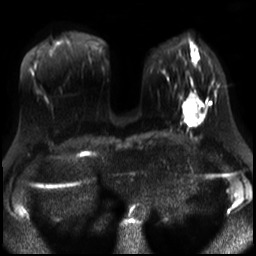
Breast MRI, one axial slice; slice 11 of 30 in the series (ordered by position); diffusion-weighted series; image 2 of 4 stored at this slice position (different b-values; order by instance number); 3 T; 256 × 256 image matrix, field of view 320 × 320 mm. Female patient.
Annotated regions visible in this slice (manually delineated by an expert):
- tumour on diffusion-weighted imaging: box from (x=183, y=93) to (x=200, y=124) px